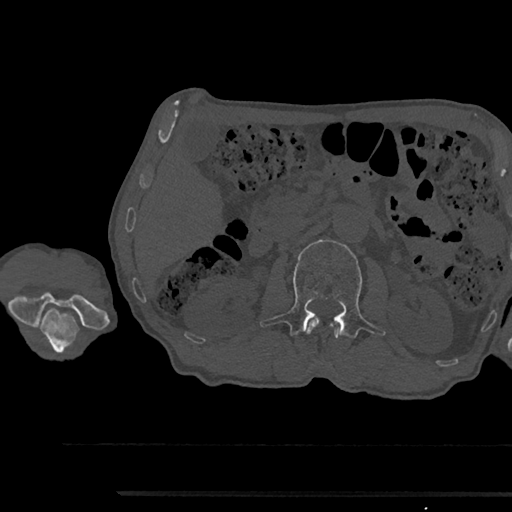
CT including the spine, one axial slice; slice 580 of 797 in the series (ordered by position); 120 kVp; bone window (W 1800 / L 400 HU); 512 × 512 image matrix, field of view 367 × 367 mm. Male patient, age 79 years. Case-level facts recorded for this patient, not image findings: primary cancer: prostate.
Outlined on this slice (semi-automatically segmented with operator editing):
- L1 vertebra: bounding box (x1, y1, x2, y2) in pixels: (307, 318, 342, 340)
- L2 vertebra: (259, 239, 385, 338)